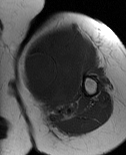
MRI of an extremity soft-tissue mass, one axial slice. Slice 52 of 86 in the series (ordered by position). MR volume resampled by the dataset authors to the PET/CT grid (not the native acquisition matrix). 3.27 mm slice thickness. 126 × 155 image matrix. Female patient. Case-level facts recorded for this patient, not image findings: histological type: pleiomorphic leiomyosarcoma; grade: high; site of the primary tumour: left biceps.
Outlined on this slice (expert contour drawn on MRI and transferred to this co-registered scan by the dataset authors):
- gross tumour volume including surrounding oedema: bounding box <22,24,91,116> (left, top, right, bottom; pixels)
- gross tumour volume (mass): <22,26,87,107>